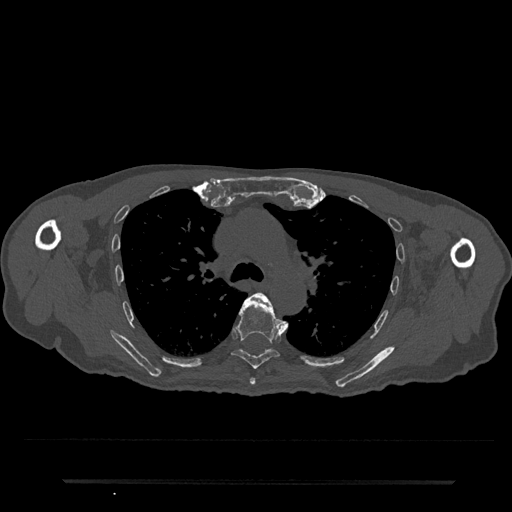
CT including the spine, one axial slice. Slice 536 of 797 in the series (ordered by position). Bone window (W 1800 / L 400 HU). 512 × 512 image matrix, field of view 427 × 427 mm. Patient: male, 74 years. From the clinical record (not read from this slice): primary cancer: prostate.
Structures marked on this image (semi-automatic segmentation, software-assisted and operator-edited):
- T5 vertebra: box from (x=250, y=293) to (x=288, y=385) px
- T6 vertebra: (x=231, y=292)–(x=282, y=369)